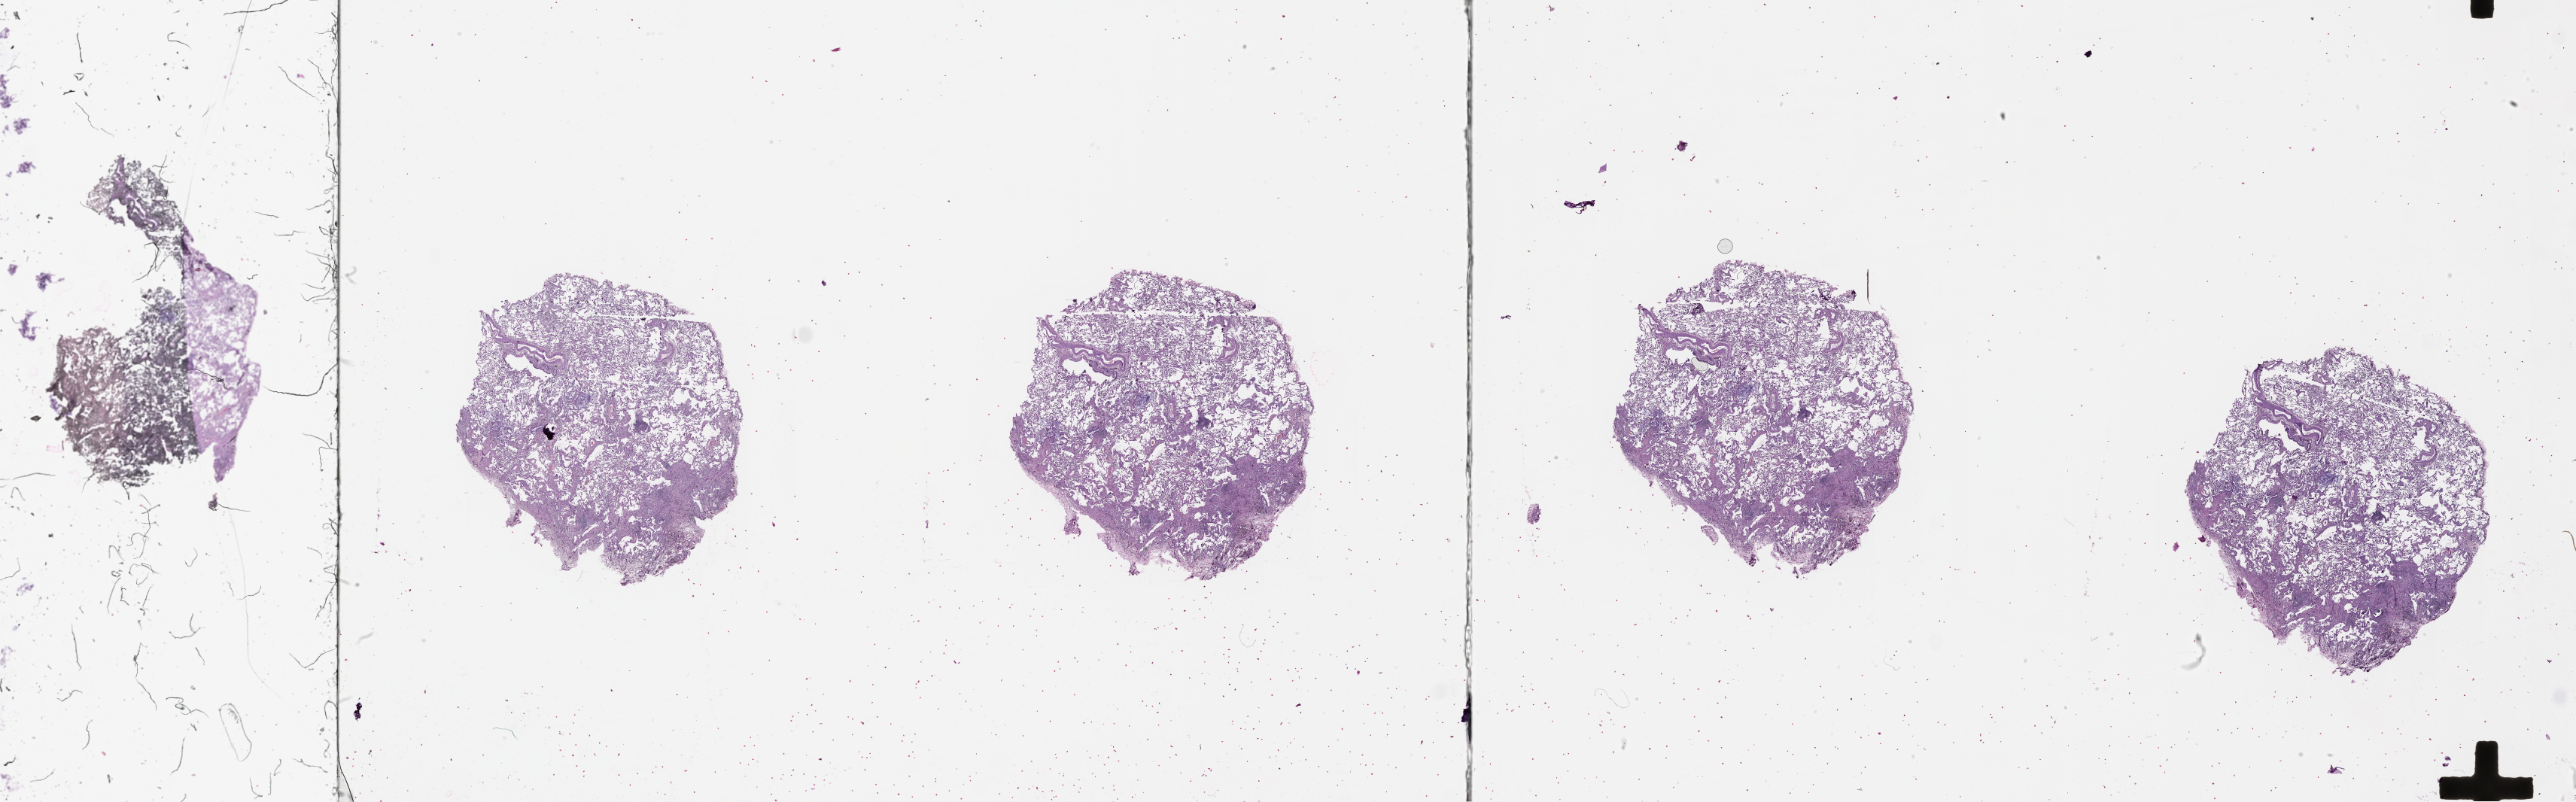
Whole-slide histology image, H&E-stained — whole scanned area (about 55.1 x 17.2 mm) shown as a low-resolution overview, lung, normal (non-tumour) tissue. Patient: male, age 67 years.
* this section: normal (non-tumour) tissue from the same patient
* patient diagnosis (cohort enrolment): squamous cell carcinoma (lung)